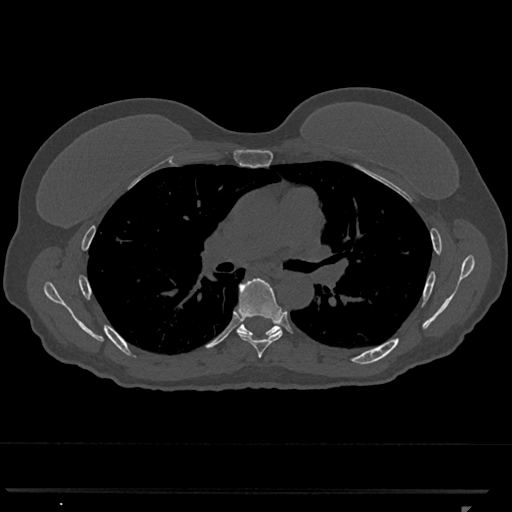
CT including the spine, one axial slice. Slice 746 of 793 in the series (ordered by position). Reconstruction kernel Br40s/3. Bone window (W 1800 / L 400 HU). 0.5 mm slice thickness. 512 × 512 image matrix. Patient: female, 62 years. Case-level facts recorded for this patient, not image findings: primary cancer: renal.
Annotated regions visible in this slice (semi-automatically segmented with operator editing):
- T6 vertebra: box from (x=237, y=278) to (x=283, y=358) px
- T7 vertebra: (x=237, y=323)–(x=279, y=337)